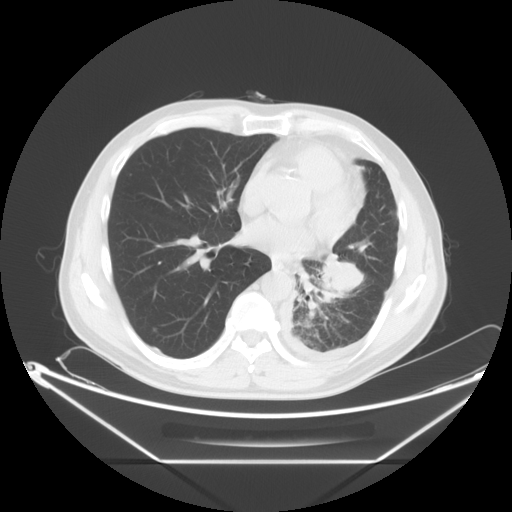
Chest CT, one axial slice. Slice 29 of 63 in the series (ordered by position). 120 kVp. Lung window (W 1500 / L -600 HU). 5 mm slice thickness. 512 × 512 image matrix. Male patient, age 60 years. From the clinical record (not read from this slice): clinical TNM (as recorded): T4 N1 M1.
Outlined on this slice (rectangle marked by the reading radiologist):
- lung tumour (recorded histology: adenocarcinoma): box from (x=299, y=239) to (x=365, y=300) px